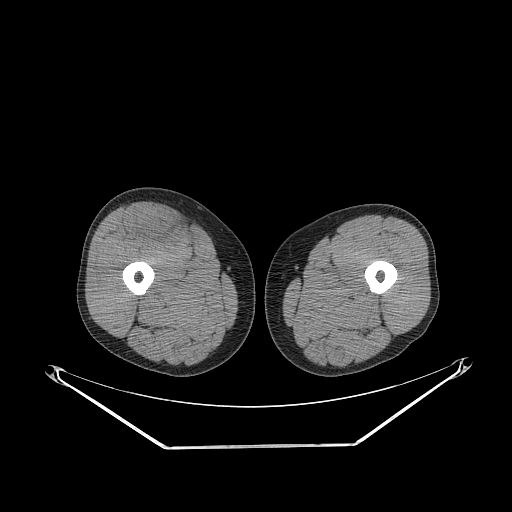
CT of an extremity soft-tissue mass (from a PET/CT study), one axial slice; position 265 of 311 along the scan axis; soft-tissue window (W 400 / L 40 HU); 3.75 mm slice thickness; 512 × 512 image matrix, field of view 500 × 500 mm. Male patient. Case-level facts recorded for this patient, not image findings: histological type: pleiomorphic leiomyosarcoma; grade: intermediate; site of the primary tumour: right thigh.
Annotated regions visible in this slice (expert contour drawn on MRI and transferred to this co-registered scan by the dataset authors):
- gross tumour volume including surrounding oedema: bounding box <126,208,181,243> (left, top, right, bottom; pixels)
- gross tumour volume (mass): <139,215,175,241>